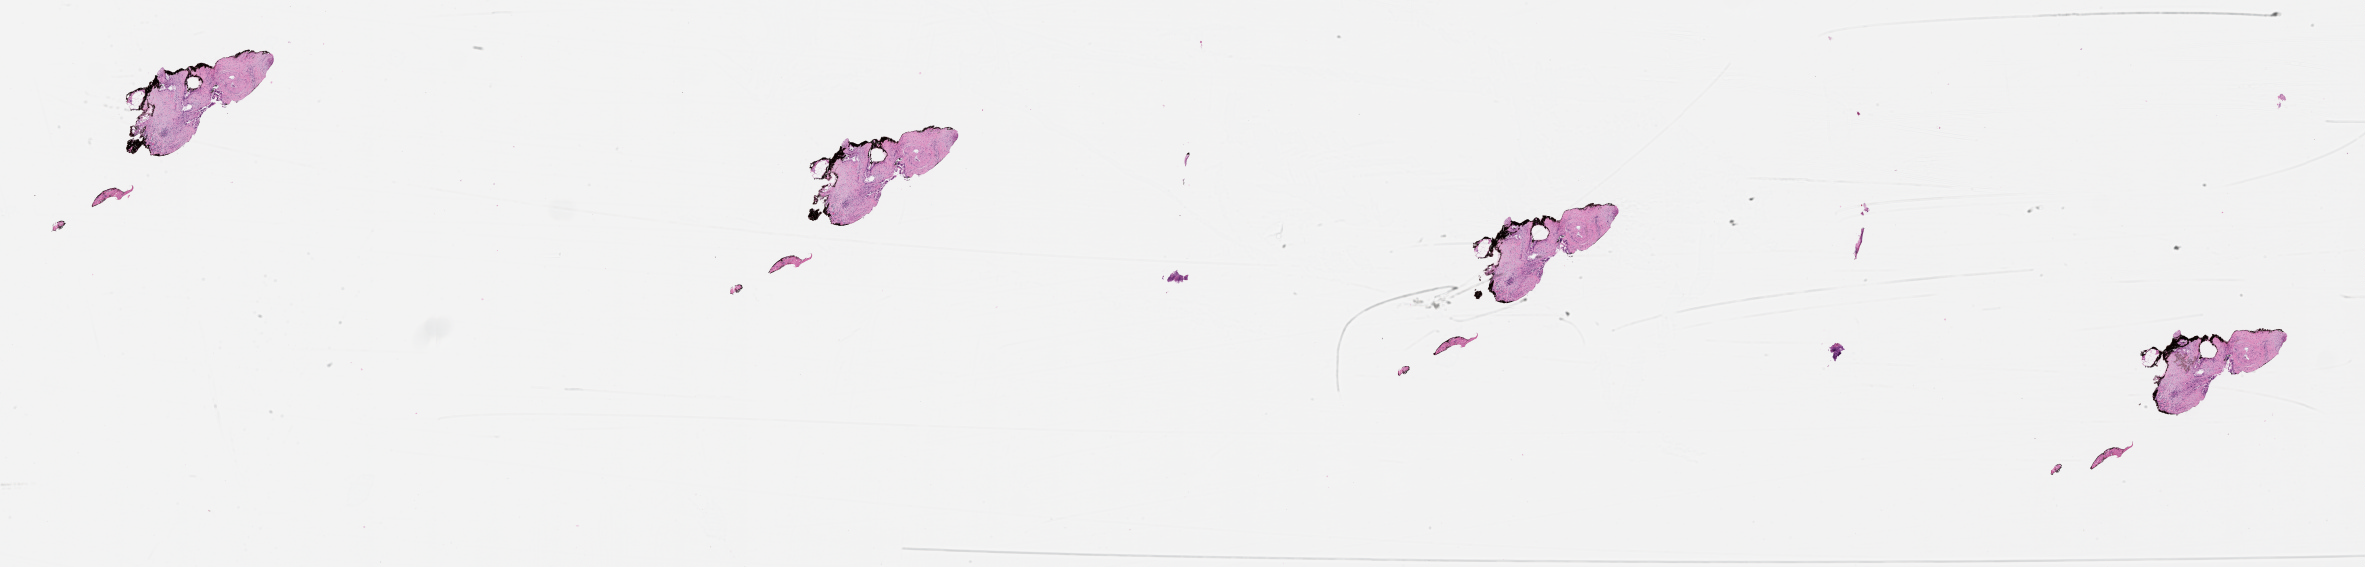
Digitized H&E tissue section (whole slide), a low-resolution overview of the entire scanned area, about 38.1 x 9.1 mm. Tumour tissue sample, sampled site: pancreas. 71-year-old female patient. Histologic grade: G3 (poorly differentiated). Composition of this section per pathologist review: tumour nuclei 20%, necrosis 0%.
• primary tumour site (as recorded): head
• diagnosis: Infiltrating duct carcinoma, NOS
• AJCC pathologic stage: IIB